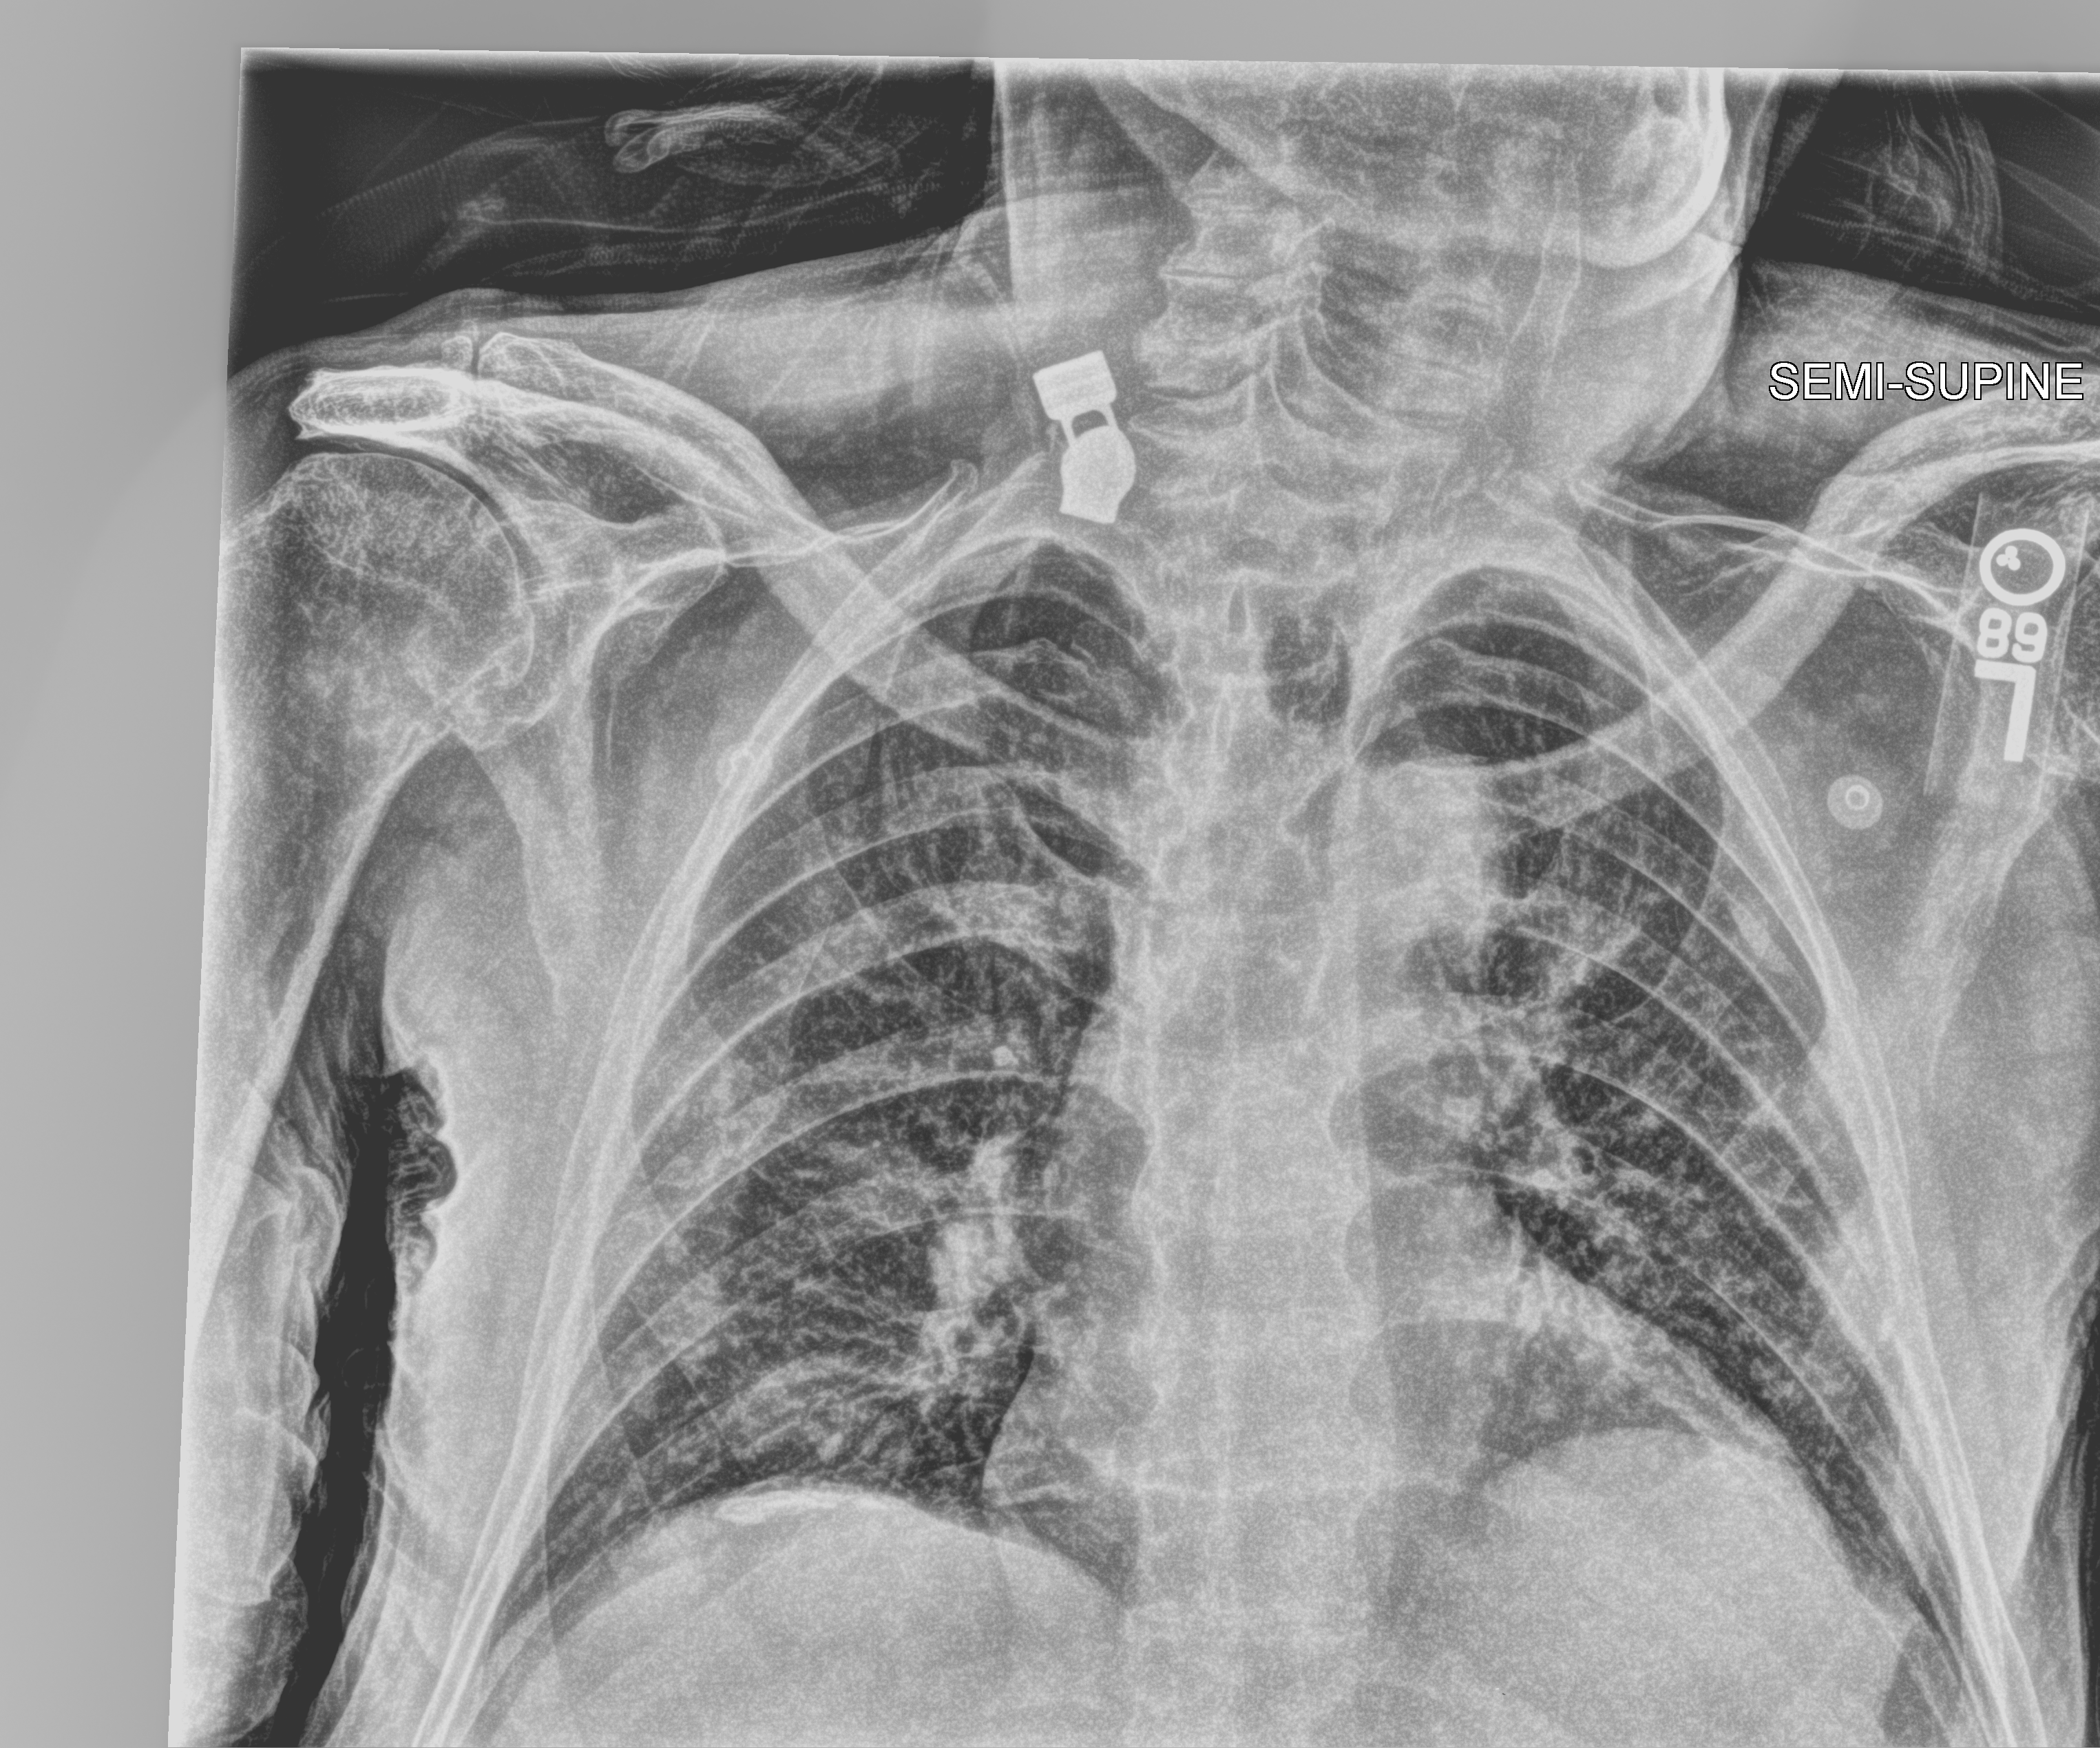
Chest X-ray (portable). Patient hospitalised with COVID-19; male, aged 75–90 years.
Admission-level facts for this patient (not findings on this image; timing relative to this image not recorded): length of hospital stay: 1 day; mechanically ventilated during this hospital stay: no.